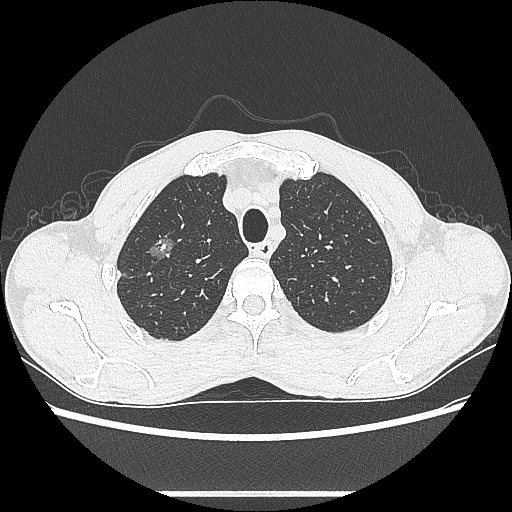
Chest CT, one axial slice; position 492 of 601 along the scan axis; reconstruction kernel LUNG; lung window (W 1500 / L -600 HU); 512 × 512 image matrix, field of view 357 × 357 mm. Male patient, age 54 years. Case-level facts recorded for this patient, not image findings: clinical TNM (as recorded): T1a N0 M0.
Annotated regions visible in this slice (rectangle marked by the reading radiologist):
- lung tumour (recorded histology: adenocarcinoma): bounding box [x1, y1, x2, y2] px = [140, 229, 184, 265]